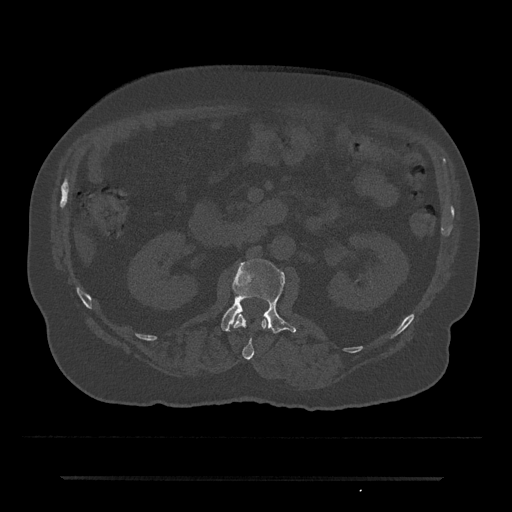
CT including the spine, one axial slice. Slice 30 of 797 in the series (ordered by position). Reconstruction kernel Br40s/3. Bone window (W 1800 / L 400 HU). 0.5 mm slice thickness. 512 × 512 image matrix, field of view 437 × 437 mm. Male patient, age 69 years. Case-level facts recorded for this patient, not image findings: primary cancer: prostate.
Outlined on this slice (semi-automatic segmentation, software-assisted and operator-edited):
- L1 vertebra: bounding box [x1, y1, x2, y2] px = [234, 314, 267, 360]
- L2 vertebra: [221, 259, 296, 334]